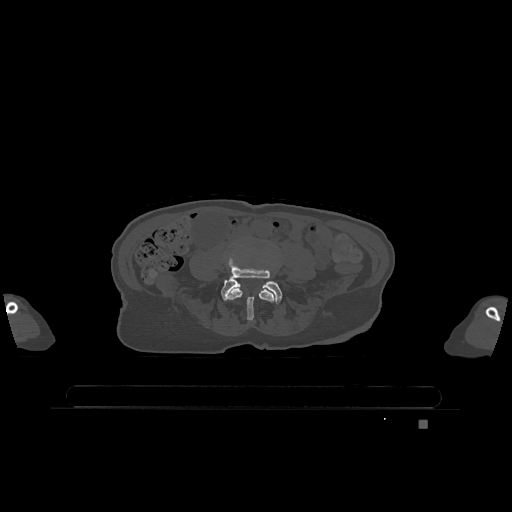
CT including the spine, one axial slice; slice 266 of 1317 in the series (ordered by position); bone window (W 1800 / L 400 HU); 0.5 mm slice thickness; 512 × 512 image matrix. Patient: female, 74 years. From the clinical record (not read from this slice): primary cancer: lung; vertebrae with lytic lesions (as recorded): T1, T4, T5, T6, L4, L5.
Annotated regions visible in this slice (semi-automatically segmented with operator editing):
- L4 vertebra: box from (x=228, y=288) to (x=274, y=321) px
- L5 vertebra: (x=221, y=266)–(x=282, y=304)